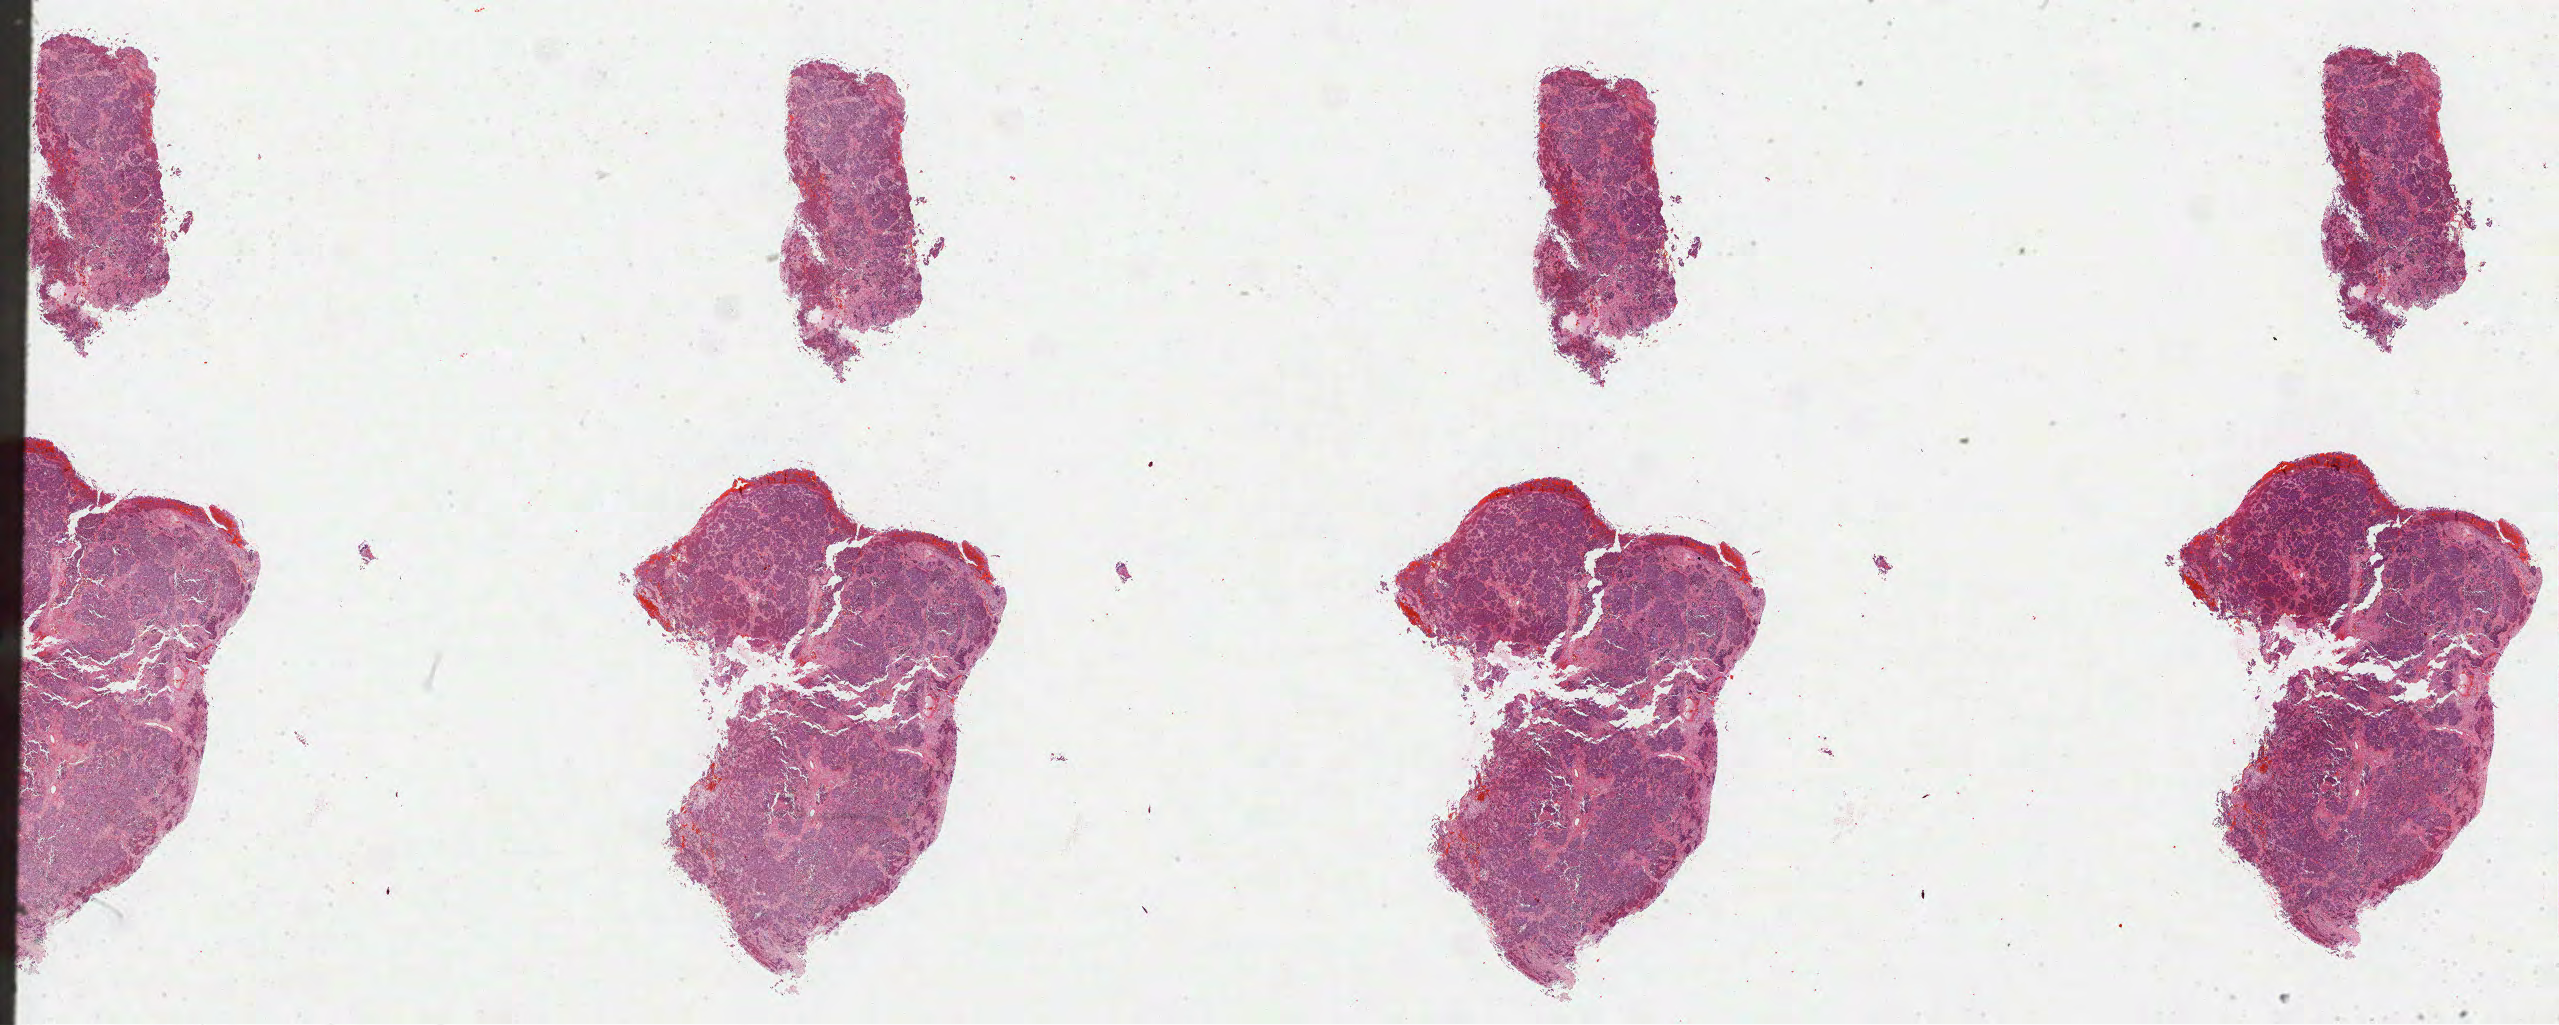
Hematoxylin and eosin (H&E) stained whole-slide image, low-resolution overview of the scanned area, about 41.2 x 16.5 mm. Formalin-fixed paraffin-embedded (FFPE) diagnostic section. Cervix, primary tumour sample. Female, age 42 years at initial diagnosis. Histologic grade: G3 (poorly differentiated).
Pathologic diagnosis: Adenocarcinoma, endocervical type (cervix uteri). FIGO stage: IB2.